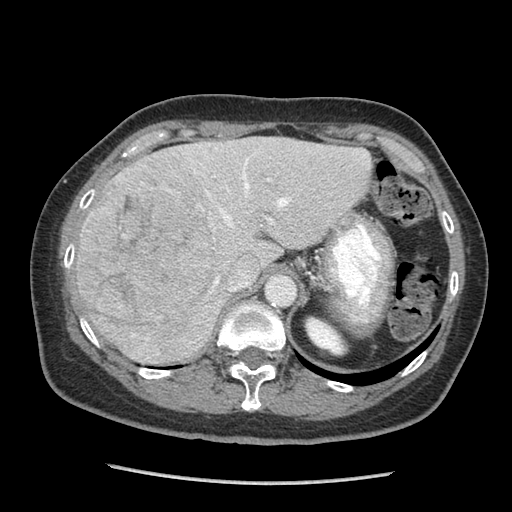
Contrast-enhanced abdominal CT (liver protocol), one axial slice; slice 61 of 105 in the series (ordered by position); reconstruction kernel STANDARD; 140 kVp; soft-tissue window (W 400 / L 40 HU); 2.5 mm slice thickness; 512 × 512 image matrix. From the clinical record (not read from this slice): diagnosis: hepatocellular carcinoma (patient treated with transarterial chemoembolisation; whether this scan precedes or follows treatment is not stated here); TNM stage (as recorded): Stage-I; Child-Pugh class: A; tumour differentiation: moderately differentiated; tumour size: 11.1 cm.
Outlined on this slice (semi-automatically segmented with operator editing):
- abdominal aorta: box from (x=267, y=275) to (x=295, y=305) px
- liver parenchyma outside the tumour (the mass and vessels are separate outlines, so this box may not span the whole liver): (x=74, y=136)–(x=372, y=364)
- mass: (x=78, y=175)–(x=220, y=341)
- liver vessels: (x=199, y=145)–(x=365, y=285)